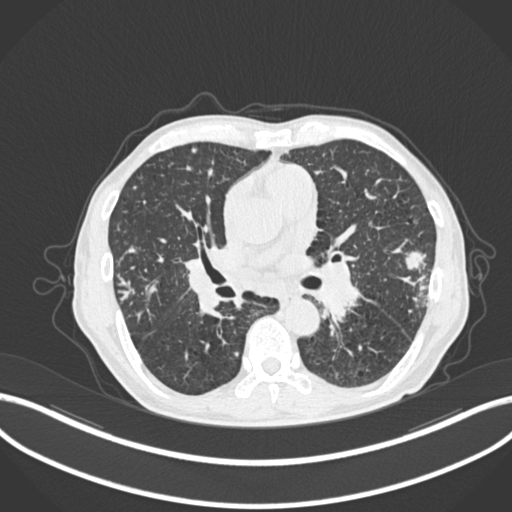
Chest CT, one axial slice; slice 121 of 287 in the series (ordered by position); lung window (W 1500 / L -600 HU); 1 mm slice thickness; 512 × 512 image matrix, field of view 400 × 400 mm. Patient: male, 74 years. Case-level facts recorded for this patient, not image findings: clinical TNM (as recorded): T2a N1 M0.
Outlined on this slice (rectangle marked by the reading radiologist):
- lung tumour (recorded histology: adenocarcinoma): box from (x=399, y=246) to (x=428, y=272) px